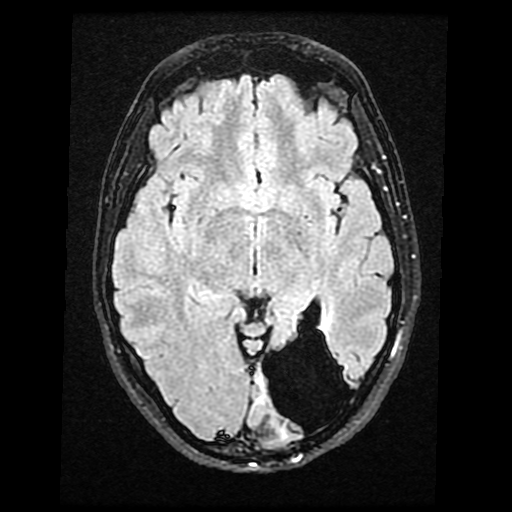
Brain MRI from a brain-tumour surgery series, one axial slice; position 23 of 40 along the scan axis; T2 FLAIR; 4 mm slice thickness; 512 × 512 image matrix, field of view 240 × 240 mm. From the clinical record (not read from this slice): histopathology: Glioma with ependymal features; WHO grade: 2.
Annotated regions visible in this slice (manually delineated by an expert):
- tumour: bounding box <277,427,289,439> (left, top, right, bottom; pixels)